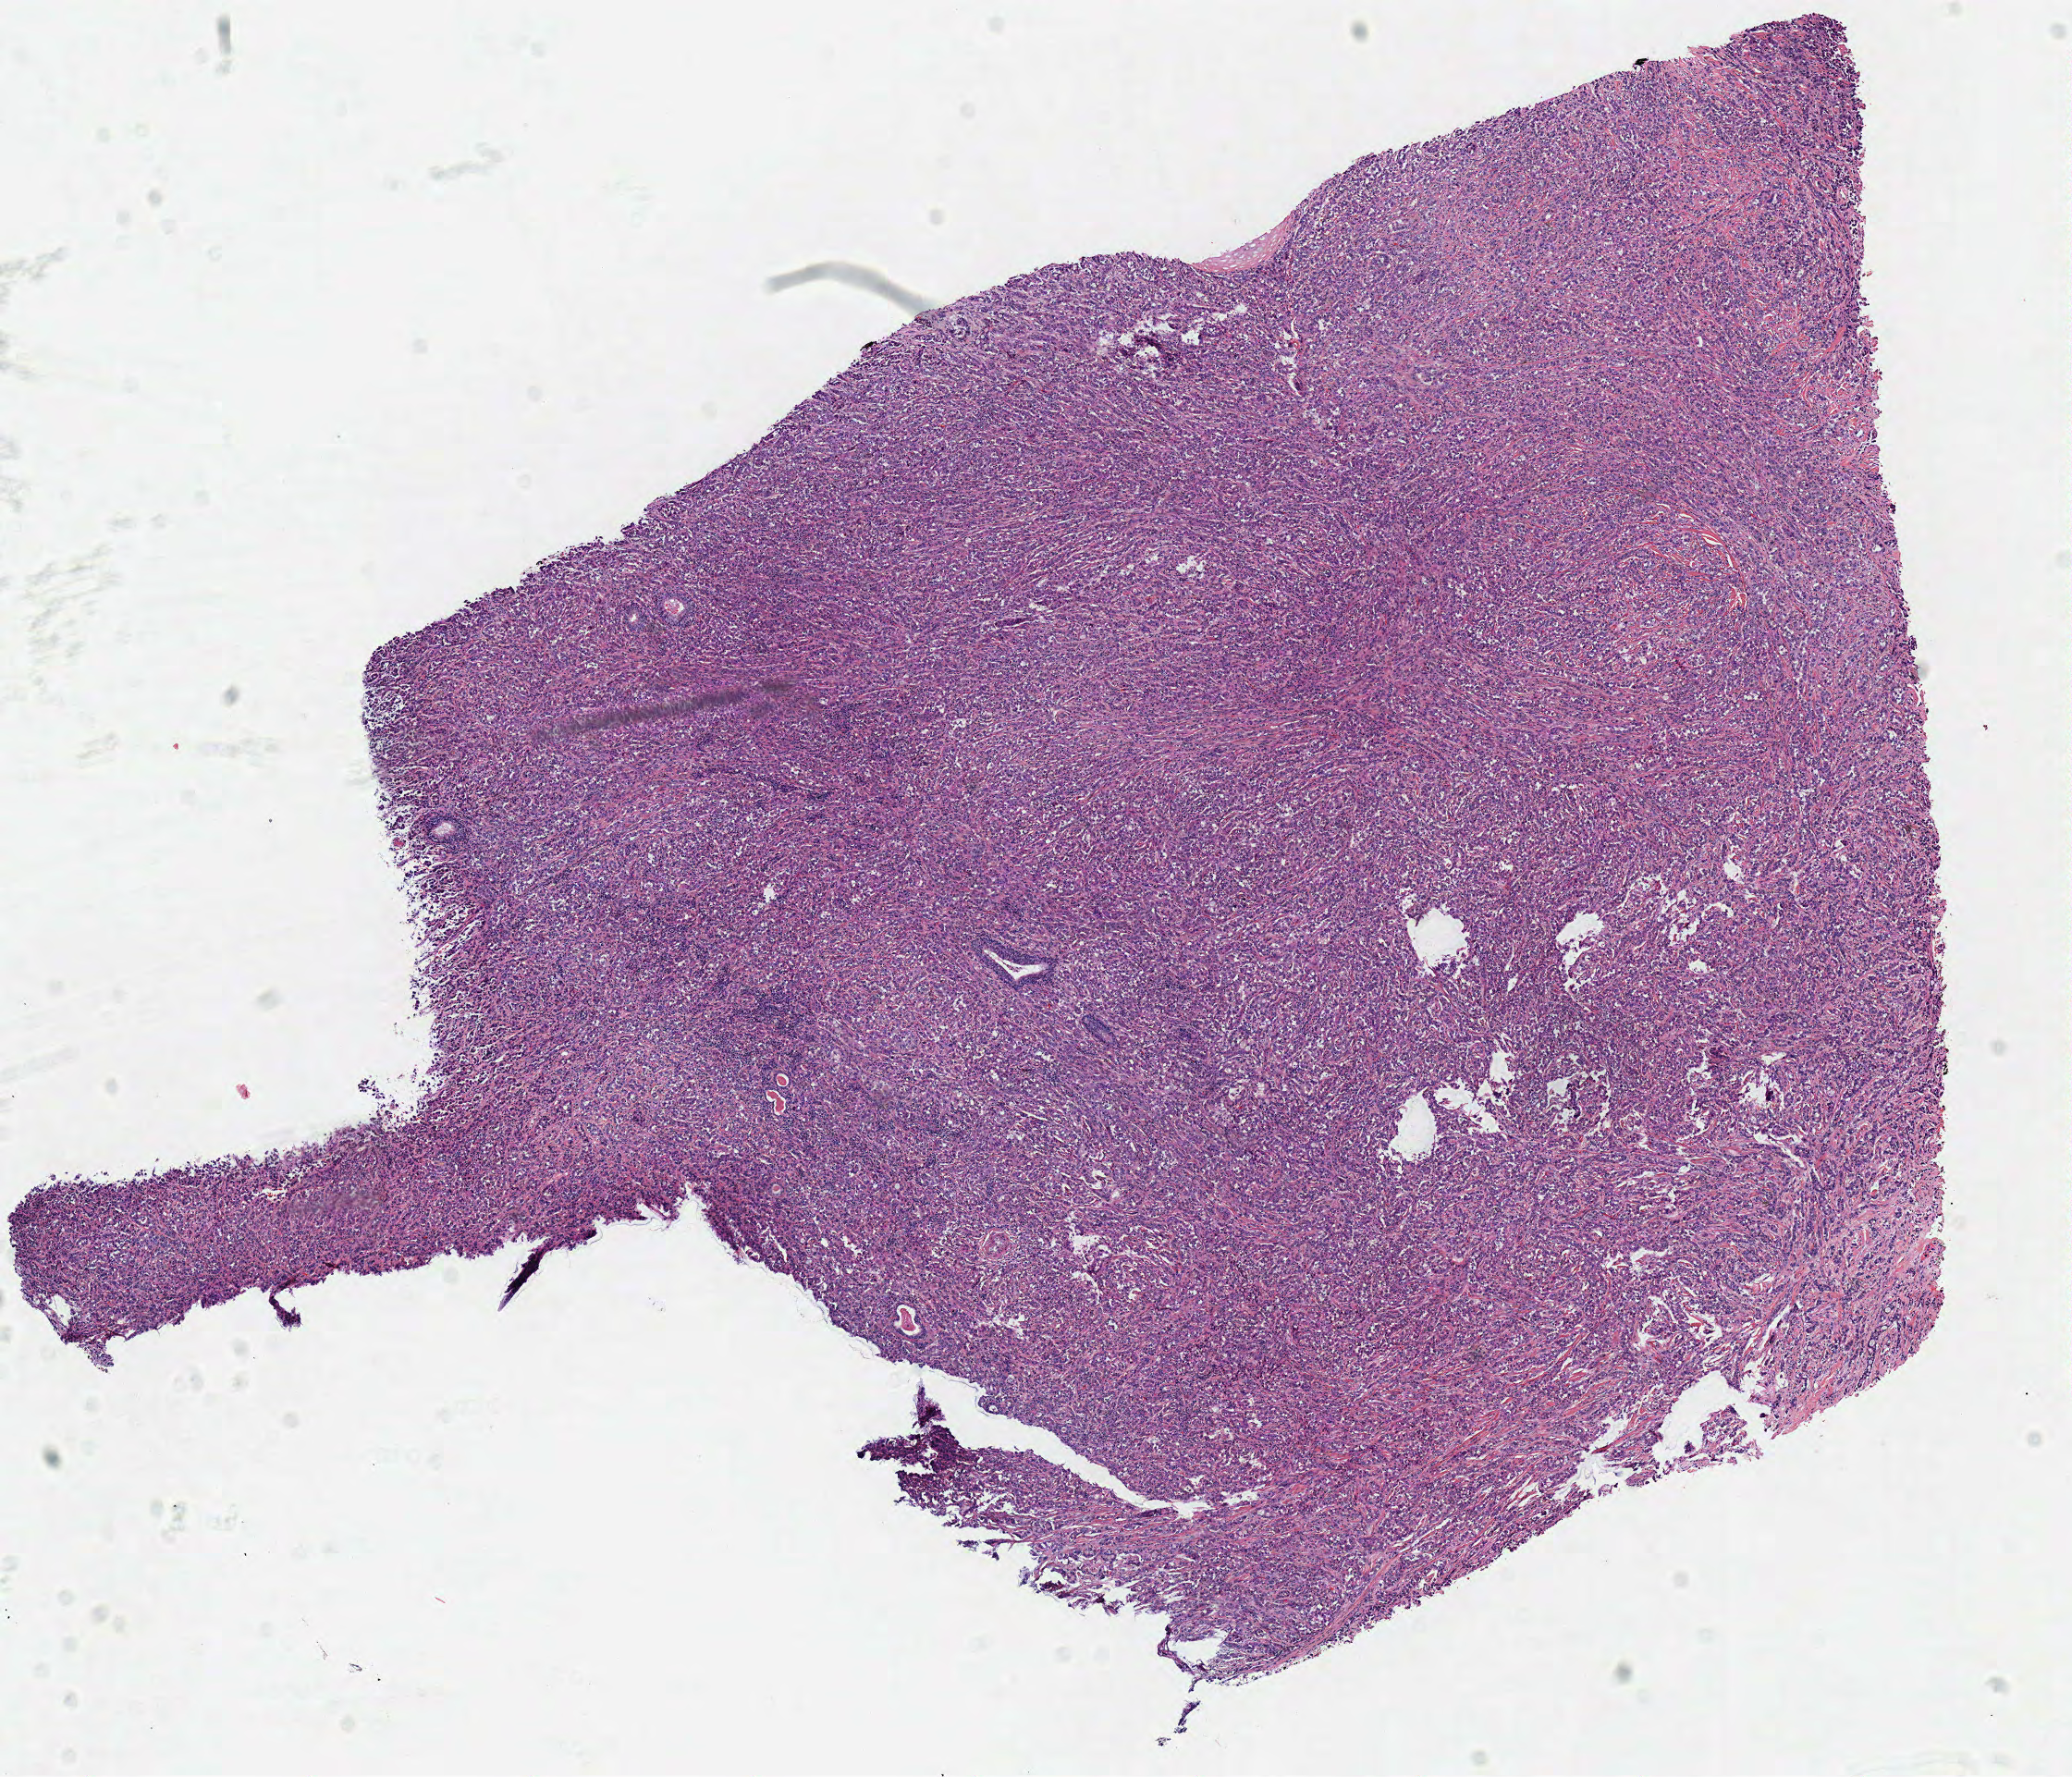
Digitized Hematoxylin and eosin (H&E) stained tissue section (whole slide) — a low-resolution overview of the entire scanned area, about 8.8 x 7.6 mm (from a 40x scan), frozen section from the top of the tissue portion, lung, primary tumour sample. Female, age 50 years at initial diagnosis. Composition of this section per pathologist review: tumour cells 100%, tumour nuclei 85%, normal cells 0%, stromal cells 0%, necrosis 0%. Infiltration values recorded for this section: lymphocyte infiltration 10%, monocyte infiltration 1%, neutrophil infiltration 2%.
* histologic diagnosis: Adenocarcinoma, NOS
* AJCC pathologic stage: IIB (6th edition)